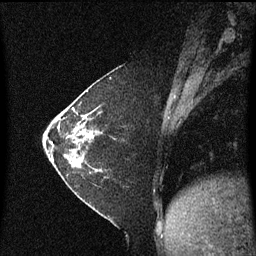
Breast MRI (dynamic contrast-enhanced), one sagittal slice. Position 21 of 60 along the scan axis. Dynamic contrast-enhanced series, image 2 of 3 at this slice position (ordered by acquisition). 1.5 T. TE 4.2 ms, TR 8.4 ms. 2 mm slice thickness. 256 × 256 image matrix, field of view 200 × 200 mm. Patient: female, 36 years. From the clinical record (not read from this slice): setting: breast cancer imaged before/during neoadjuvant chemotherapy; receptor status: HR-positive, HER2-negative.
Structures marked on this image (semi-automatically segmented with operator editing):
- analysis volume of interest (the breast-tissue region the enhancement analysis was run in; not a lesion): box from (x=66, y=102) to (x=103, y=177) px
- tumour enhancement mask (voxels above the 70 % enhancement threshold inside the analysis volume of interest): (x=84, y=118)–(x=88, y=133)